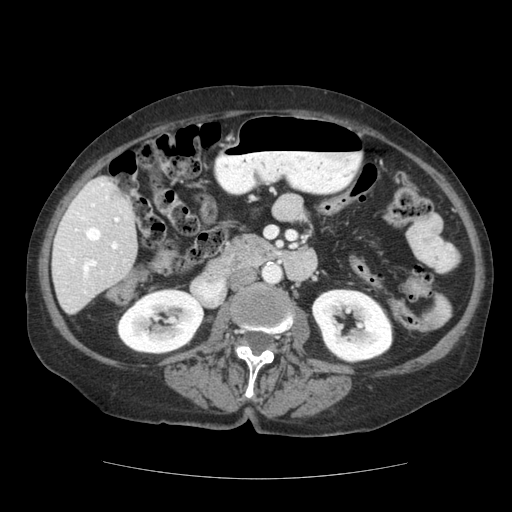
Contrast-enhanced abdominal CT (liver protocol), one axial slice. Position 51 of 111 along the scan axis. Reconstruction kernel STANDARD. 140 kVp. Soft-tissue window (W 400 / L 40 HU). 2.5 mm slice thickness. 512 × 512 image matrix. Case-level facts recorded for this patient, not image findings: diagnosis: hepatocellular carcinoma (patient treated with transarterial chemoembolisation; whether this scan precedes or follows treatment is not stated here); TNM stage (as recorded): Stage-I; Child-Pugh class: A.
Outlined on this slice (semi-automatically segmented with operator editing):
- liver parenchyma outside the tumour (the mass and vessels are separate outlines, so this box may not span the whole liver): box from (x=52, y=176) to (x=137, y=314) px
- liver vessels: (x=60, y=183)–(x=127, y=301)